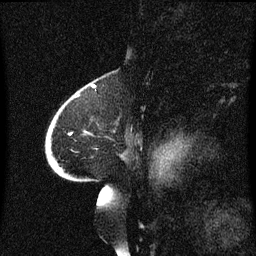
Breast MRI (dynamic contrast-enhanced), one sagittal slice; position 43 of 60 along the scan axis; dynamic contrast-enhanced series, image 2 of 3 at this slice position (ordered by acquisition); 1.5 T; TE 4.2 ms, TR 8.4 ms; 2 mm slice thickness; 256 × 256 image matrix, field of view 200 × 200 mm. Patient: female, 68 years. From the clinical record (not read from this slice): setting: breast cancer imaged before/during neoadjuvant chemotherapy; receptor status: triple-negative.
Annotated regions visible in this slice (semi-automatically segmented with operator editing):
- analysis volume of interest (the breast-tissue region the enhancement analysis was run in; not a lesion): bounding box (x1, y1, x2, y2) in pixels: (47, 94, 125, 173)
- tumour enhancement mask (voxels above the 70 % enhancement threshold inside the analysis volume of interest): (59, 168, 63, 171)